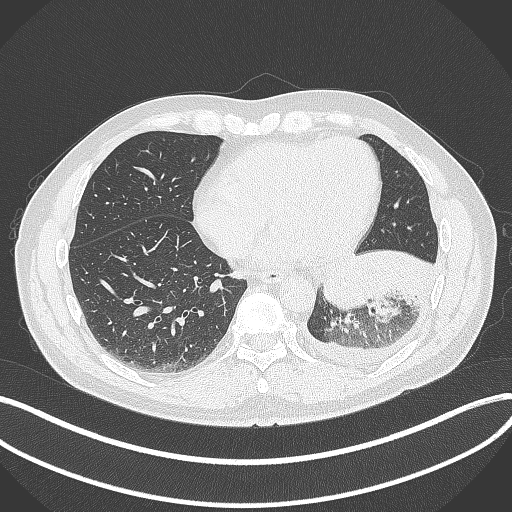
Chest CT, one axial slice; slice 118 of 342 in the series (ordered by position); reconstruction kernel B70f; 120 kVp; lung window (W 1500 / L -600 HU); 1 mm slice thickness; 512 × 512 image matrix, field of view 400 × 400 mm. Patient: male, 58 years. From the clinical record (not read from this slice): clinical TNM (as recorded): T3 N1 M1b; histopathological grade: G3.
Annotated regions visible in this slice (rectangle marked by the reading radiologist):
- lung tumour (recorded histology: small cell carcinoma): box from (x=325, y=253) to (x=371, y=318) px